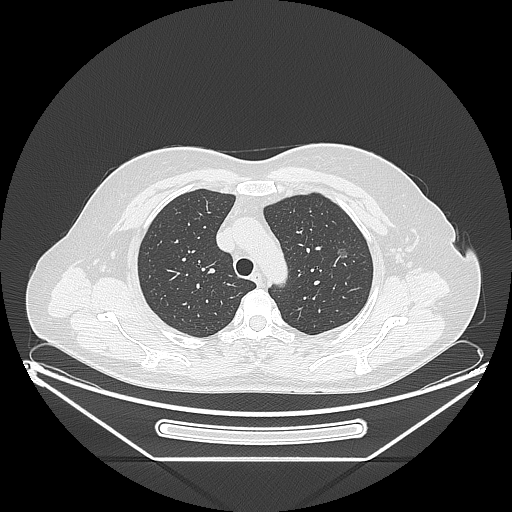
Chest CT, one axial slice; slice 168 of 226 in the series (ordered by position); lung window (W 1500 / L -600 HU); 512 × 512 image matrix, field of view 447 × 447 mm. Patient: female, 54 years. Case-level facts recorded for this patient, not image findings: clinical TNM (as recorded): T1c N0 M0.
Structures marked on this image (bounding box drawn by a radiologist):
- lung tumour (recorded histology: adenocarcinoma): box from (x=326, y=235) to (x=353, y=267) px